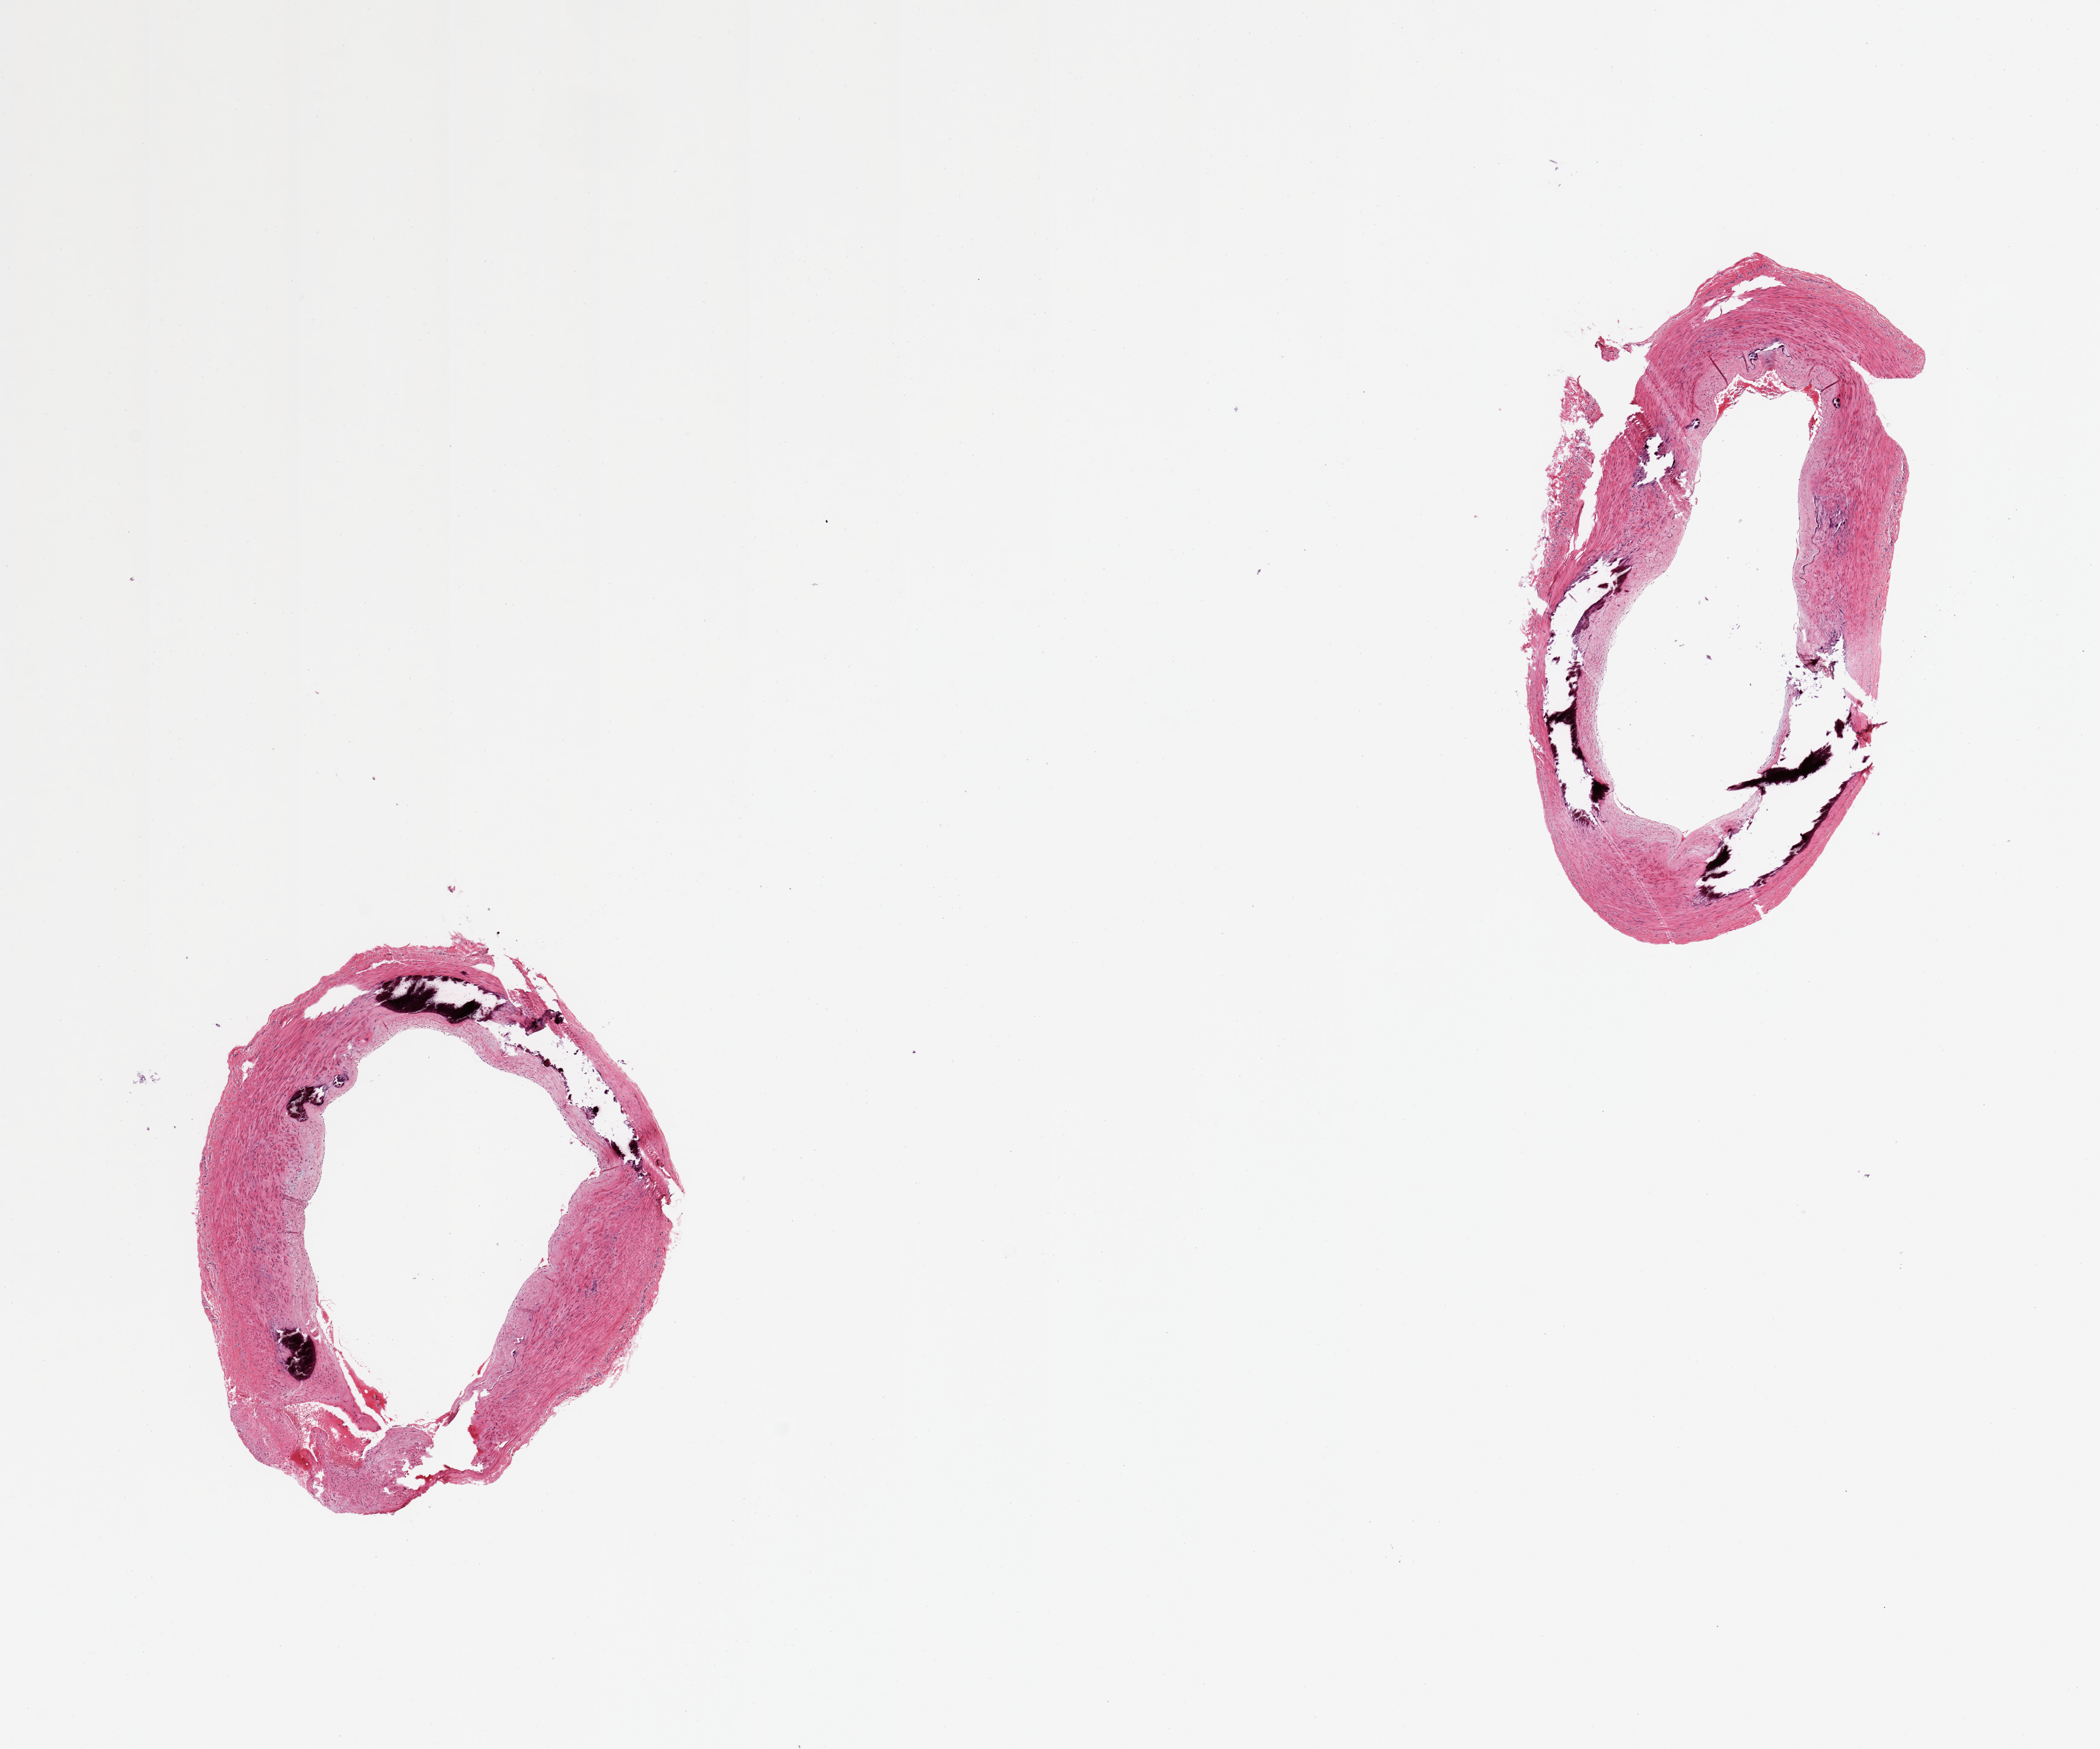
Digitized hematoxylin and eosin (H&E)-stained section — shown as a low-resolution overview of the whole scanned area (about 13.8 x 11.5 mm, slide scanned at 20x); PAXgene-fixed paraffin-embedded (PFPE) section; target tissue: tibial artery; donor tissue sample.
* pathologist's review note for this sample: 2 pieces, no significant atherosis or adherent fat; prominent Monkeberg medial sclerosis